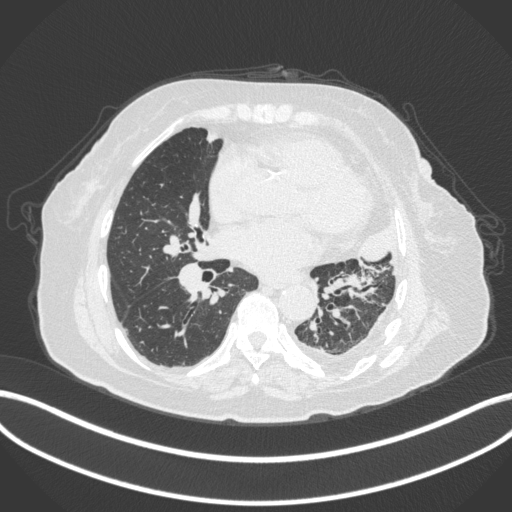
Chest CT, one axial slice. Position 170 of 399 along the scan axis. Reconstruction kernel B31f. 120 kVp. Lung window (W 1500 / L -600 HU). 1 mm slice thickness. 512 × 512 image matrix. Patient: female, 75 years. From the clinical record (not read from this slice): clinical TNM (as recorded): T3 N3 M1.
Outlined on this slice (rectangle marked by the reading radiologist):
- lung tumour (recorded histology: adenocarcinoma): bounding box (x1, y1, x2, y2) in pixels: (358, 220, 401, 271)